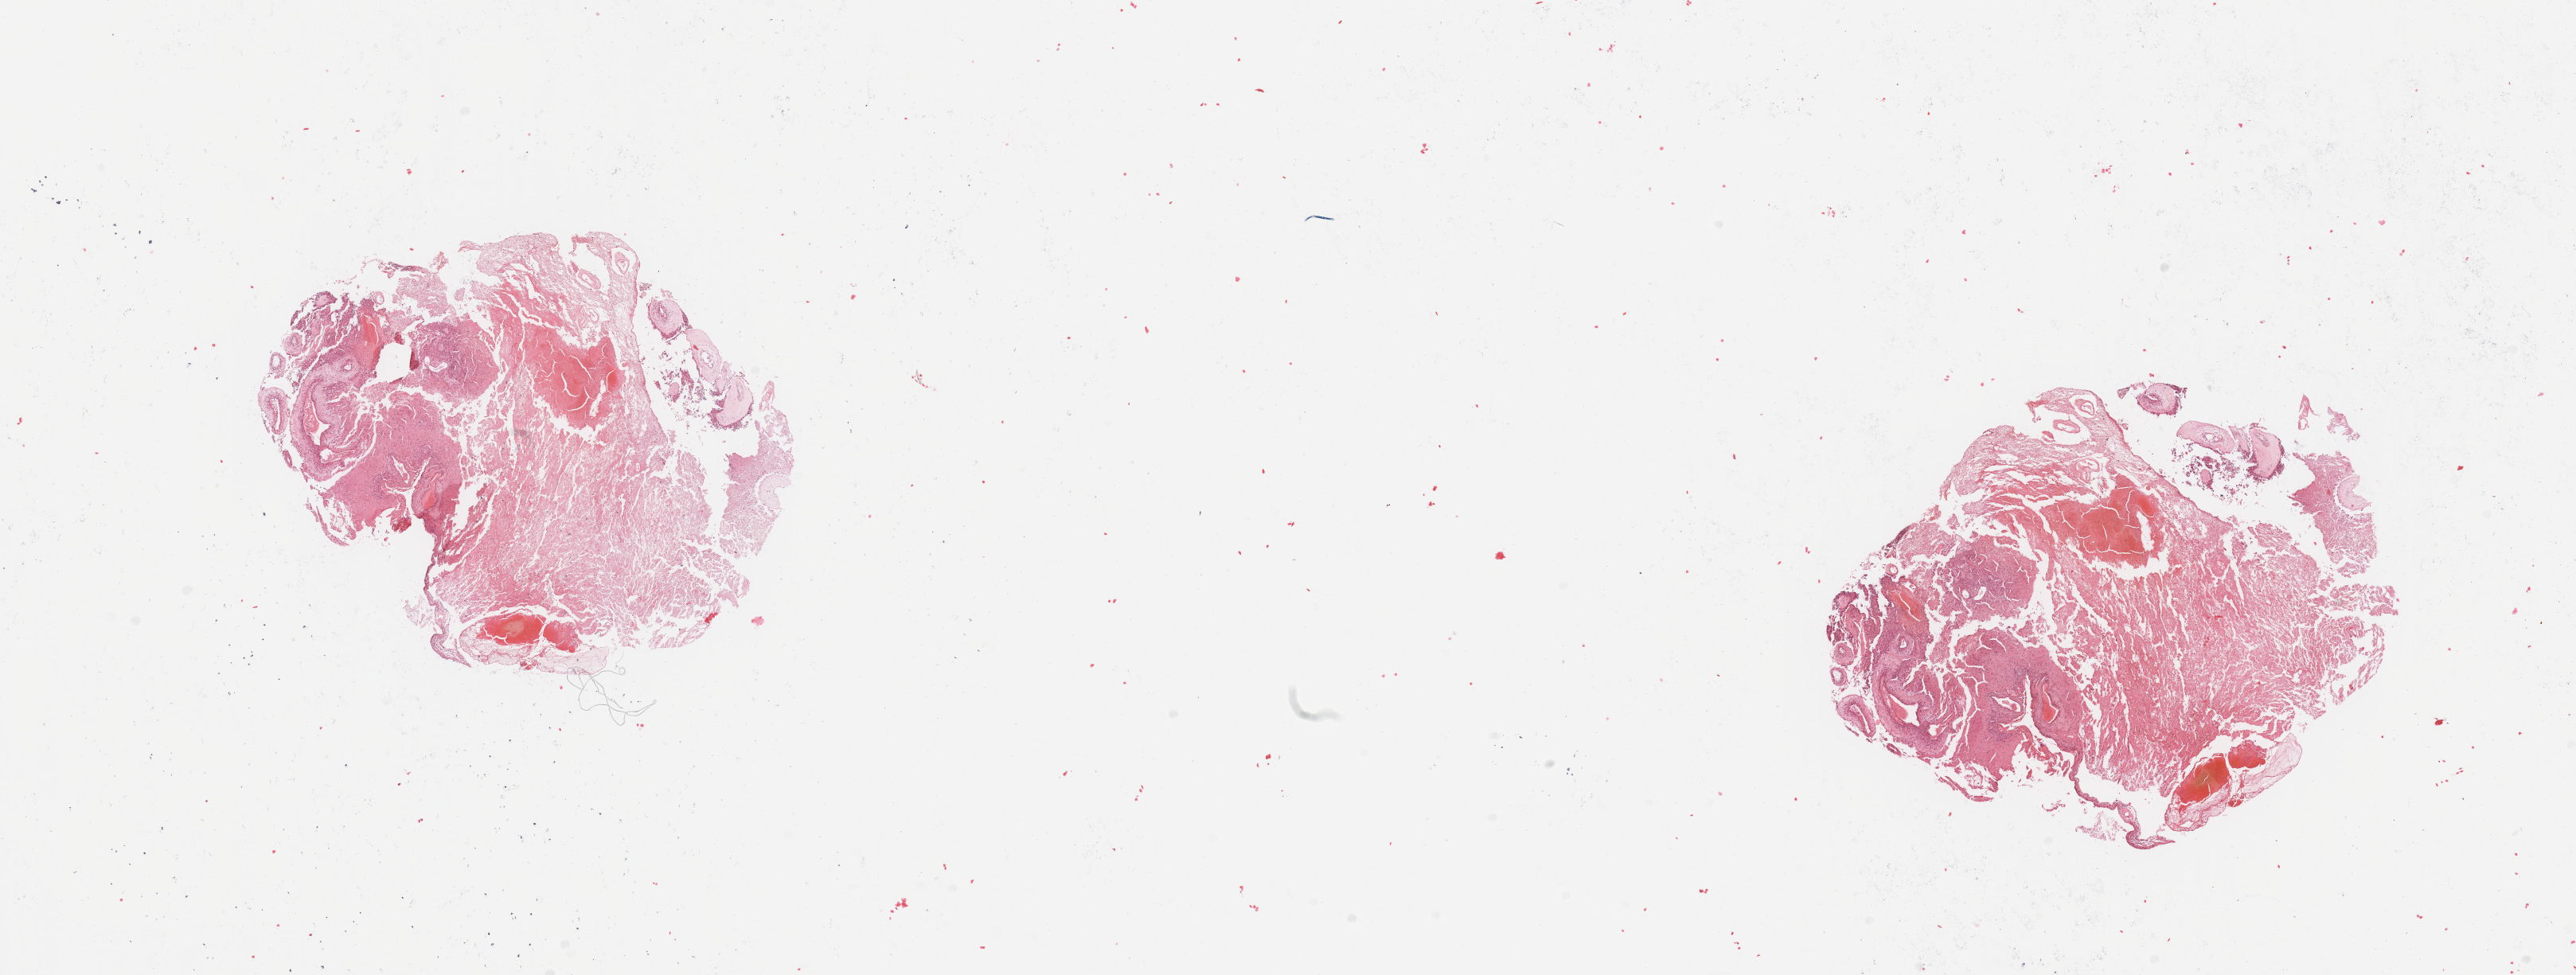
Hematoxylin and eosin (H&E) stained whole-slide image, shown as a low-resolution overview of the whole scanned area (about 25.6 x 9.7 mm); tumour tissue sample, sampled site: brain. Patient: male, age 80 years. Composition of this section per pathologist review: tumour nuclei 70%, necrosis 30%.
Primary tumour site (as recorded): temporal lobe. Histologic diagnosis: Glioblastoma.